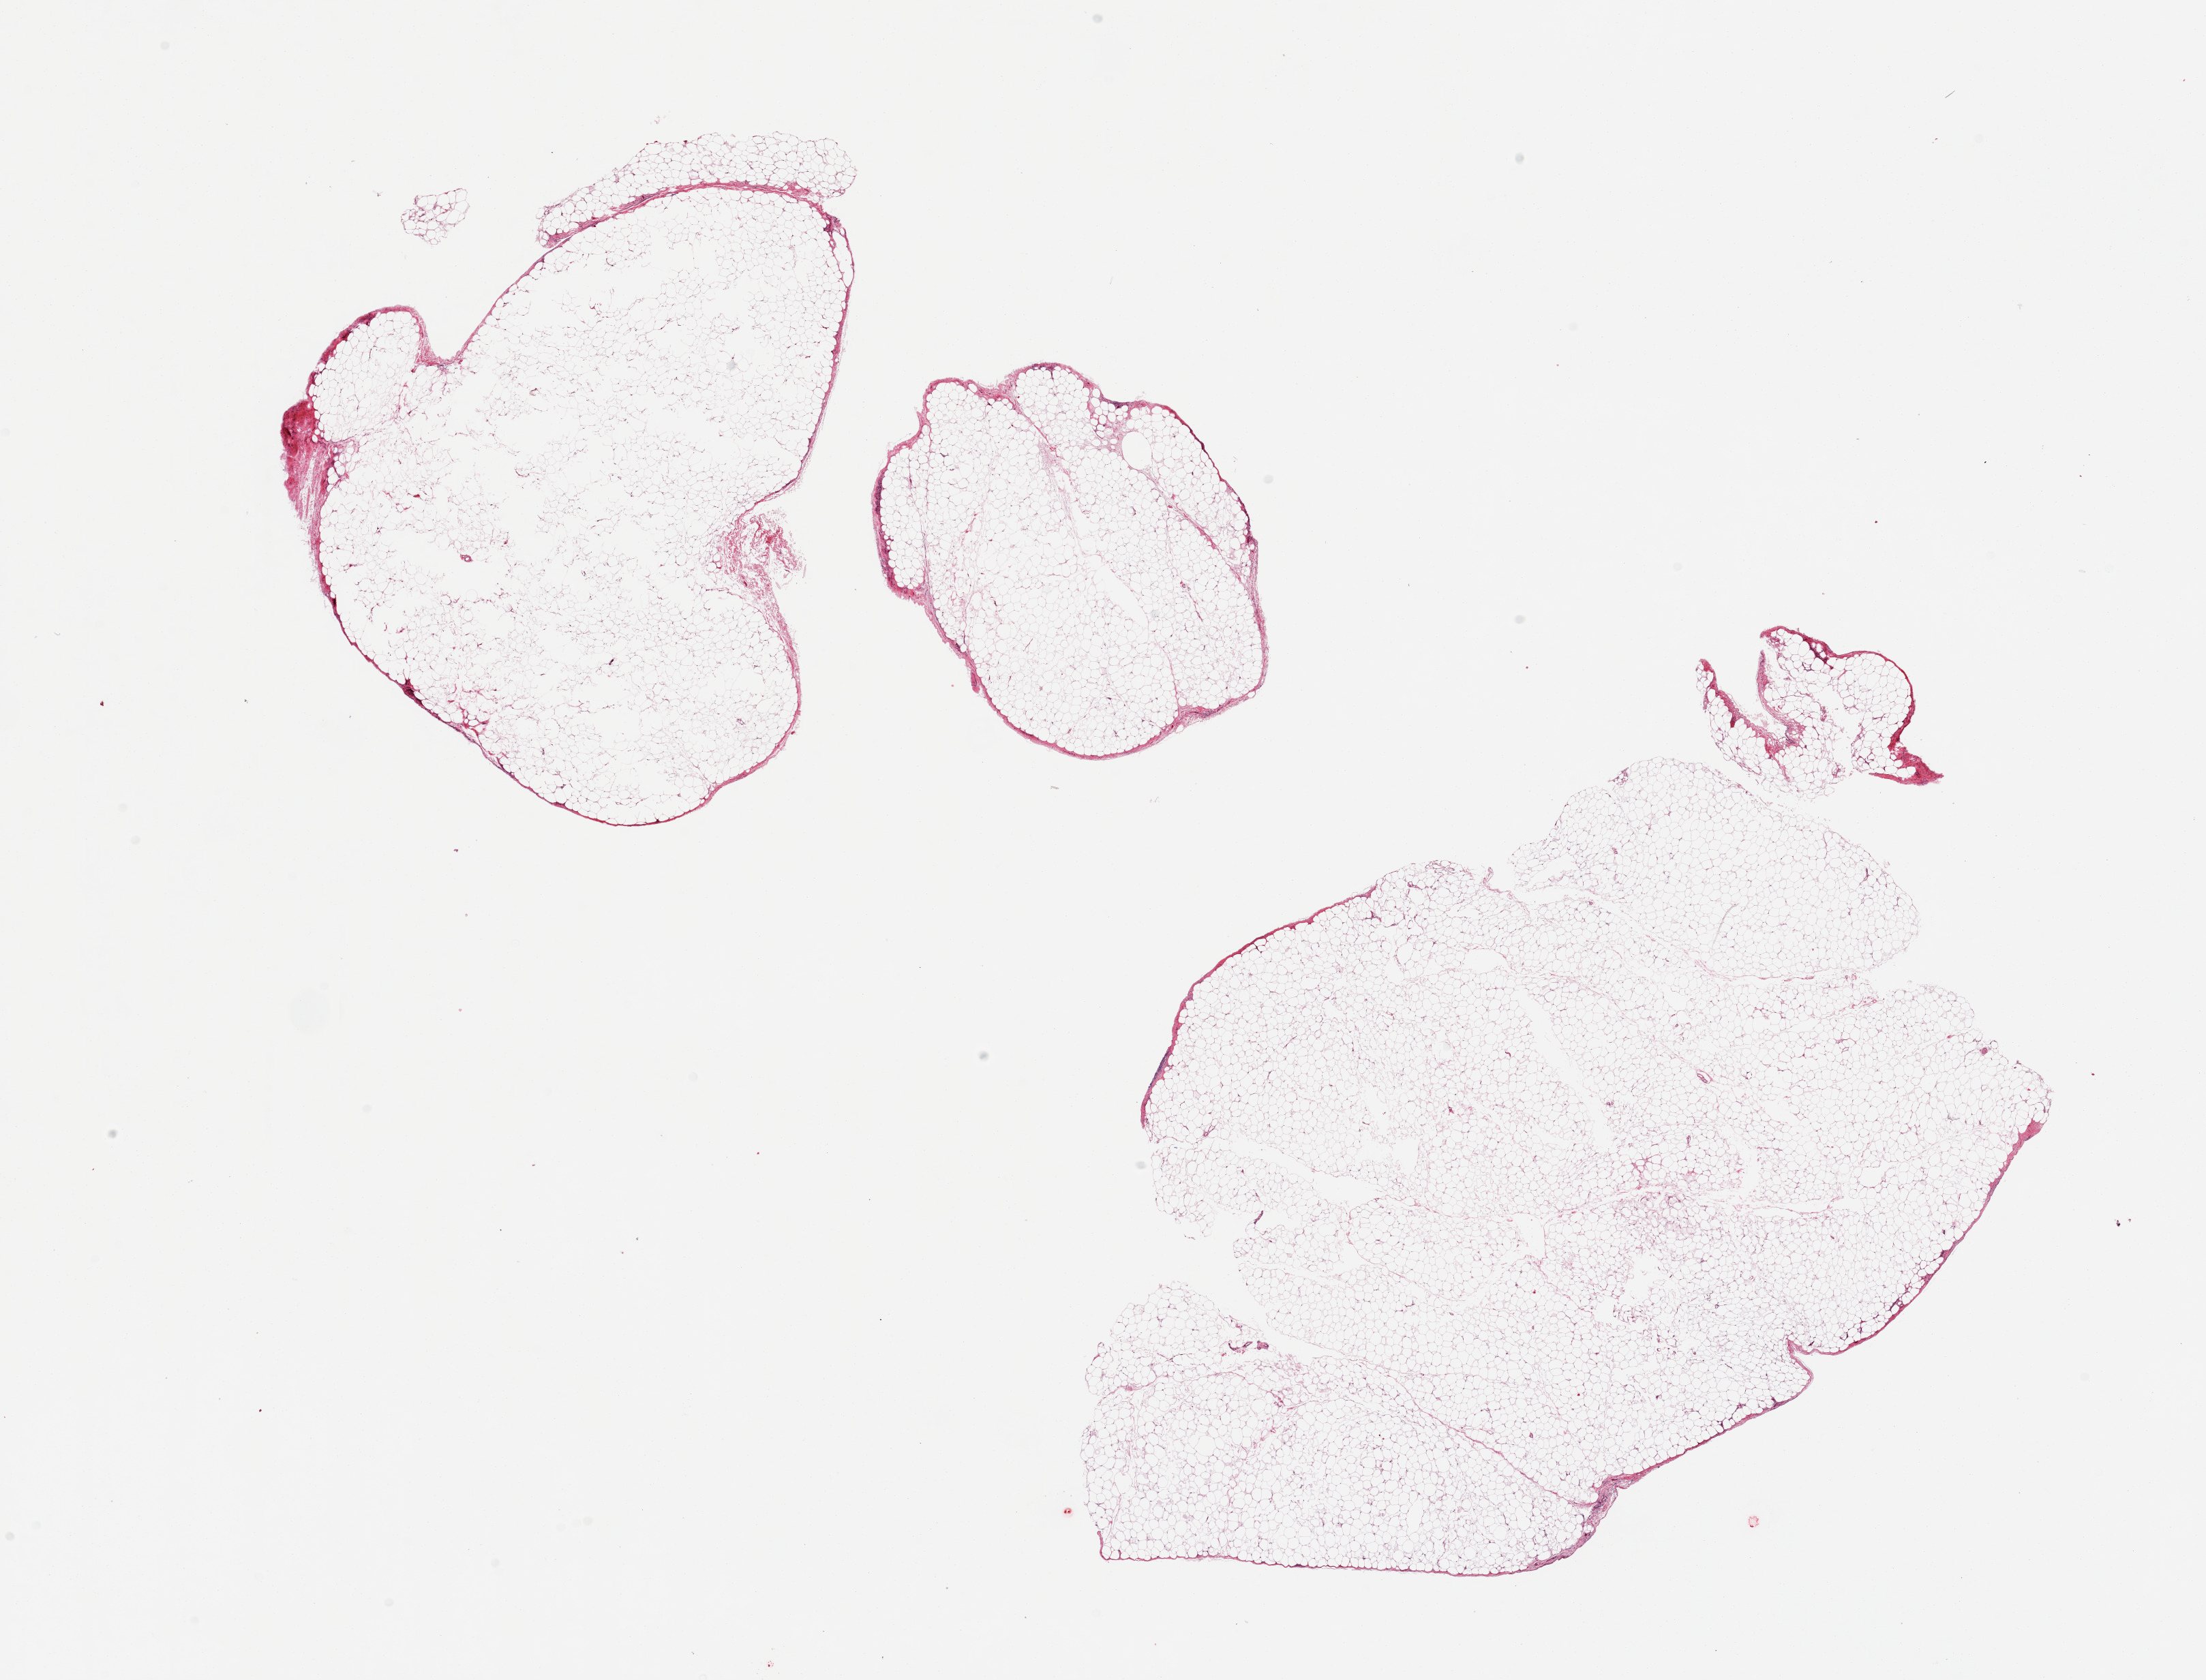
Digitized hematoxylin and eosin (H&E)-stained section — whole scanned area (about 25.6 x 19.5 mm, from a 20x scan) shown as a low-resolution overview. PAXgene-fixed paraffin-embedded (PFPE) section. Sampled site (target tissue): omentum. Donor tissue sample. Donor: female.
Reviewer comment on this tissue sample: 3 pieces, virtually all fat with only peripheral rim of fibroconnective tissue, some central defects (poor fixation) in one piece.